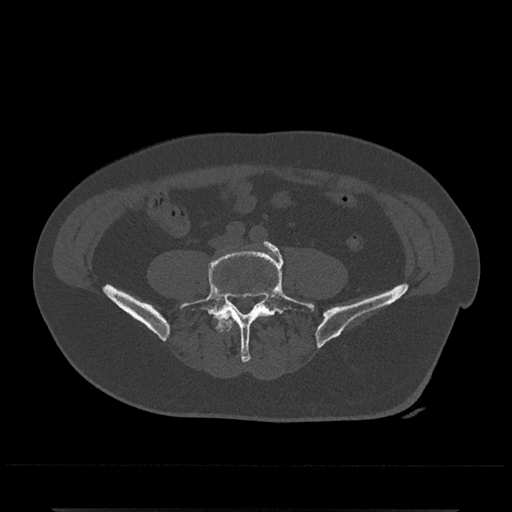
CT including the spine, one axial slice; slice 97 of 797 in the series (ordered by position); reconstruction kernel Br40s/3; 120 kVp; bone window (W 1800 / L 400 HU); 0.5 mm slice thickness; 512 × 512 image matrix. Patient: male, 67 years. Case-level facts recorded for this patient, not image findings: primary cancer: prostate.
Outlined on this slice (semi-automatic segmentation, software-assisted and operator-edited):
- L4 vertebra: bounding box [x1, y1, x2, y2] px = [220, 318, 234, 332]
- L5 vertebra: [180, 241, 315, 362]